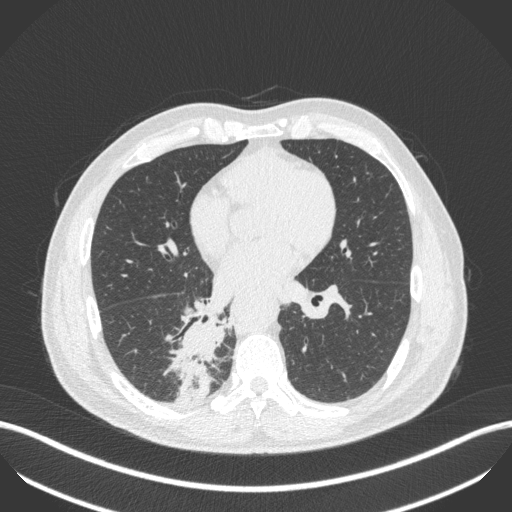
Chest CT, one axial slice. Slice 218 of 451 in the series (ordered by position). 100 kVp. Lung window (W 1500 / L -600 HU). 1 mm slice thickness. 512 × 512 image matrix, field of view 400 × 400 mm. Patient: male, 61 years. From the clinical record (not read from this slice): clinical TNM (as recorded): T1 N0 M0; histopathological grade: G3.
Structures marked on this image (rectangle marked by the reading radiologist):
- lung tumour (recorded histology: small cell carcinoma): bounding box [x1, y1, x2, y2] px = [175, 317, 224, 411]